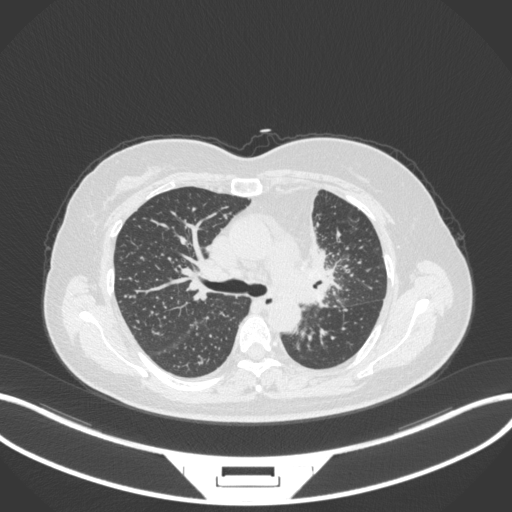
Chest CT, one axial slice. Position 215 of 348 along the scan axis. 120 kVp. Lung window (W 1500 / L -600 HU). 1 mm slice thickness. 512 × 512 image matrix, field of view 400 × 400 mm. Female patient, age 49 years. From the clinical record (not read from this slice): clinical TNM (as recorded): T1c N0 M1.
Structures marked on this image (rectangle marked by the reading radiologist):
- lung tumour (recorded histology: adenocarcinoma): bounding box <293,215,342,309> (left, top, right, bottom; pixels)